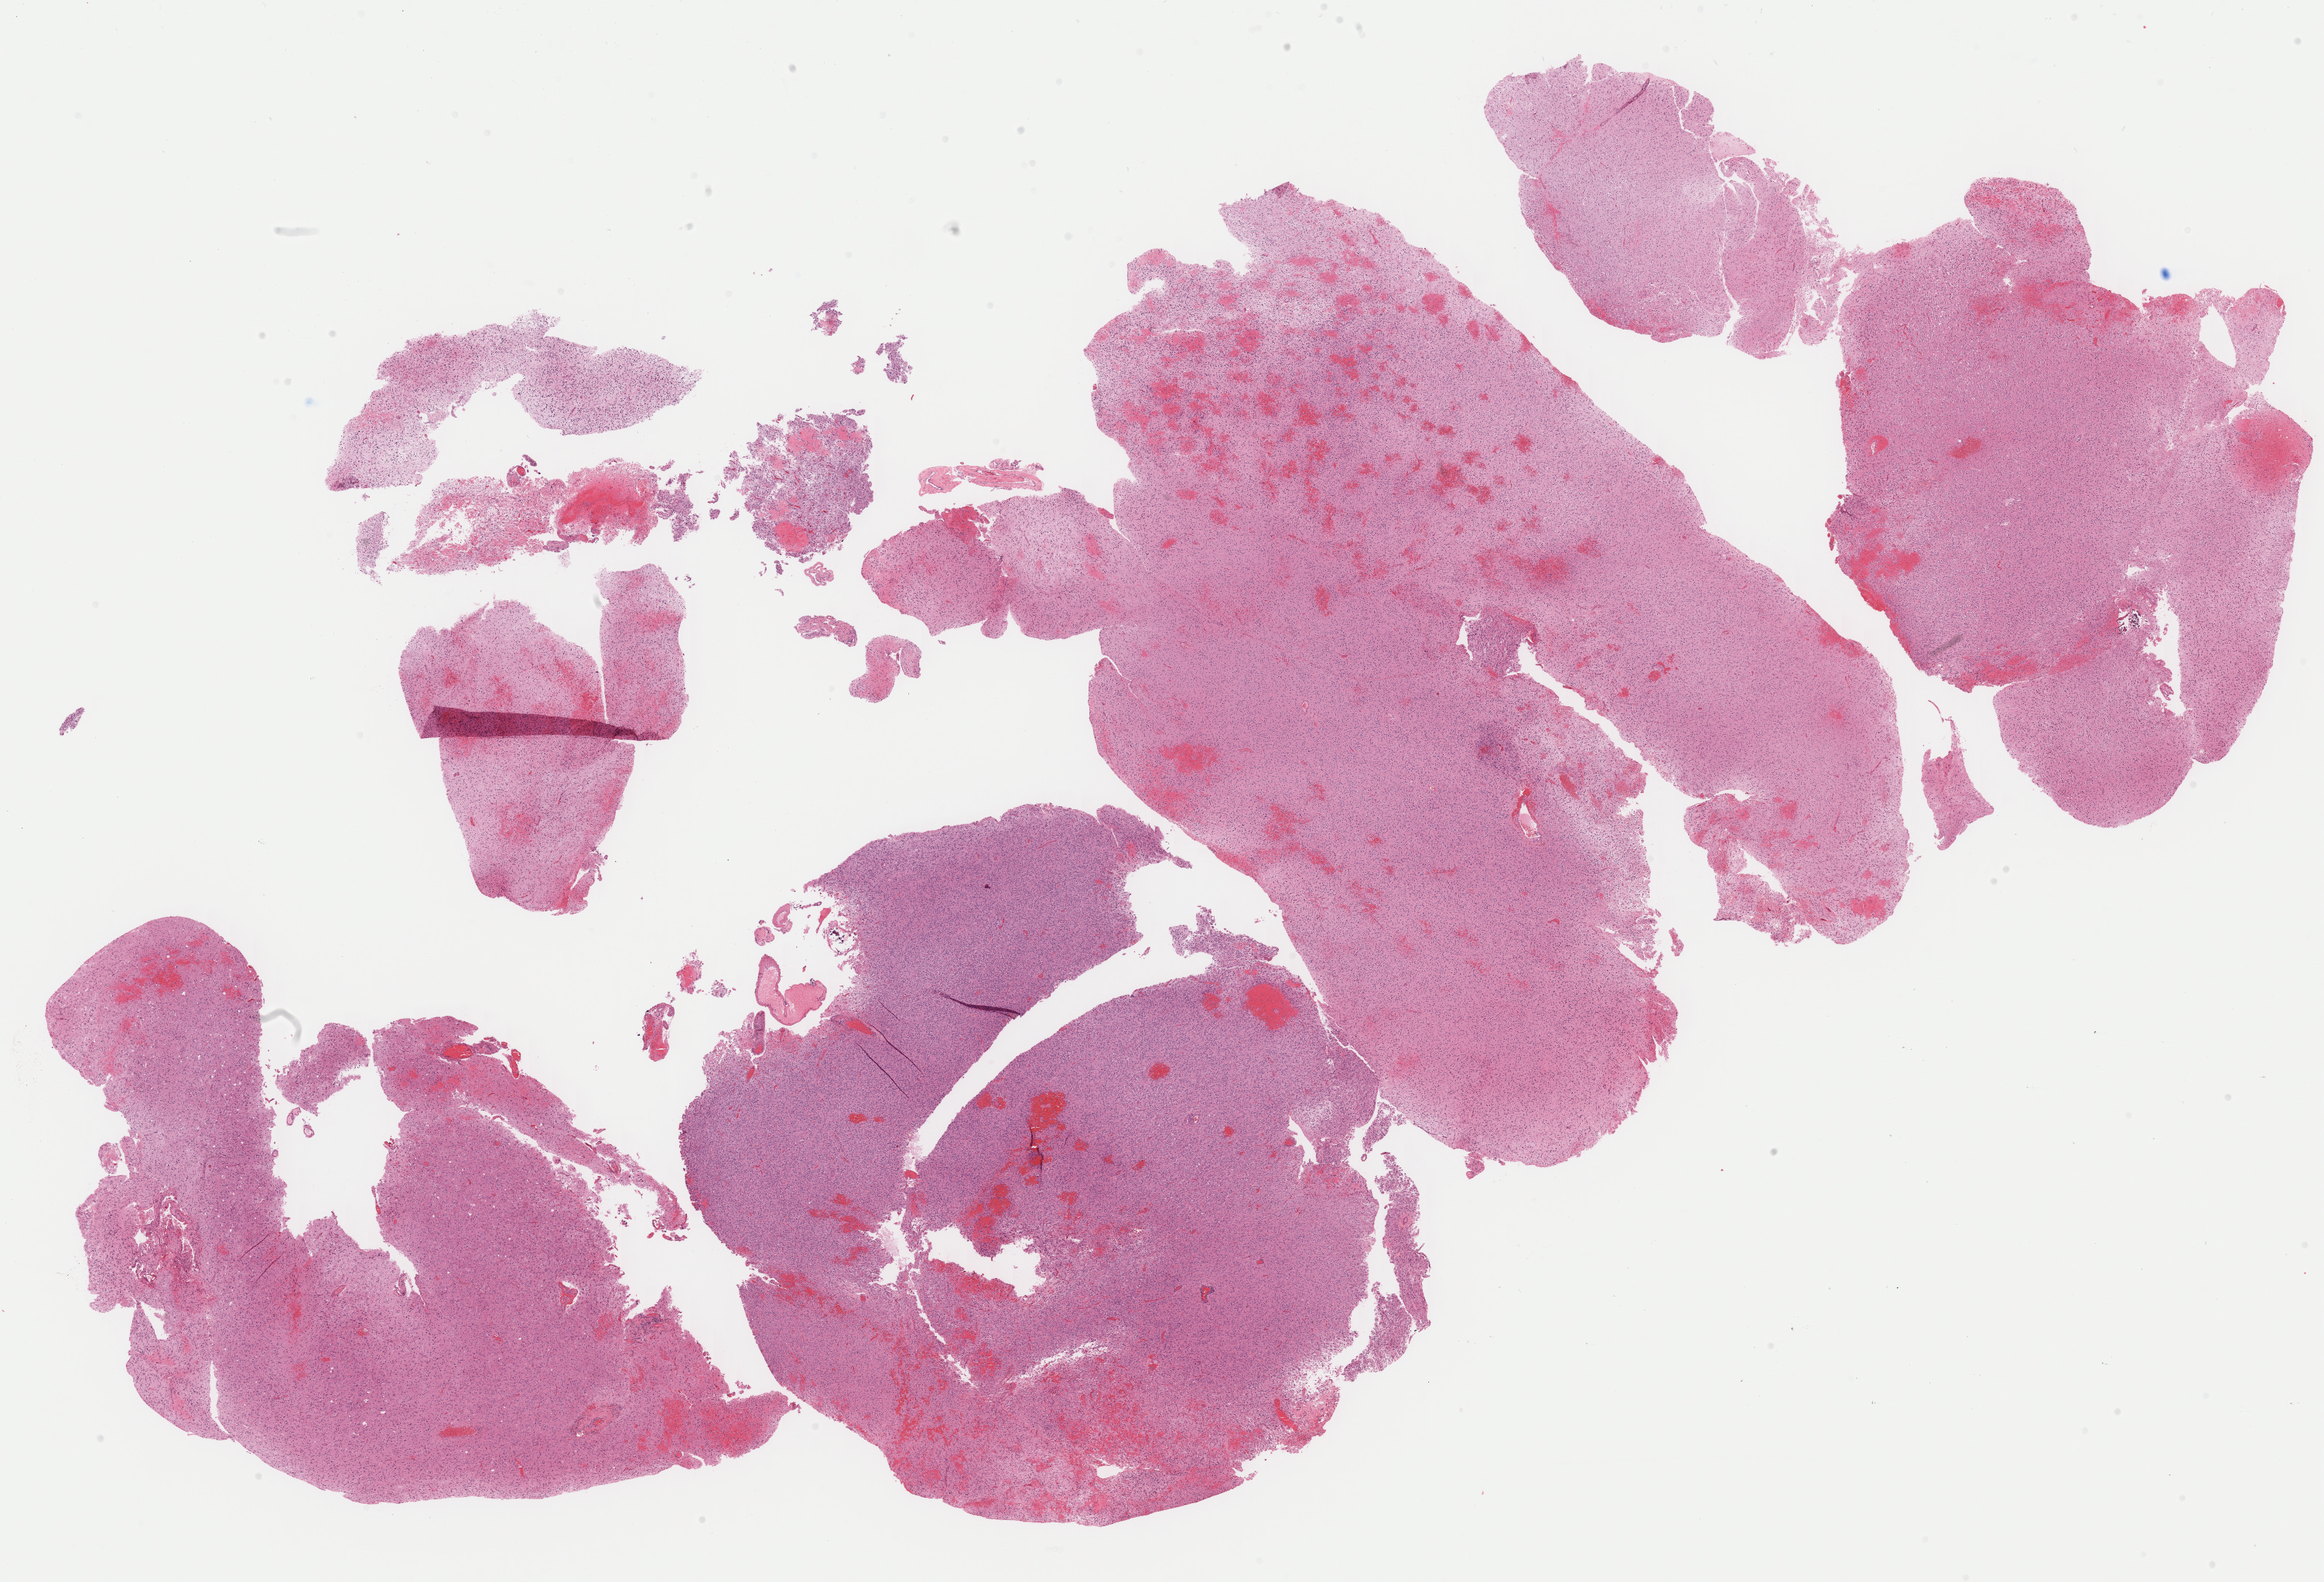
Digitized H&E tissue section (whole slide) — shown as a low-resolution overview of the whole scanned area (about 23.7 x 16.1 mm, slide scanned at 40x), formalin-fixed paraffin-embedded (FFPE) diagnostic section, sample: primary tumour, brain. Male, age 32 years at initial diagnosis. Histologic grade: G3 (poorly differentiated).
* laterality: left
* pathologic diagnosis: Mixed glioma (cerebrum)